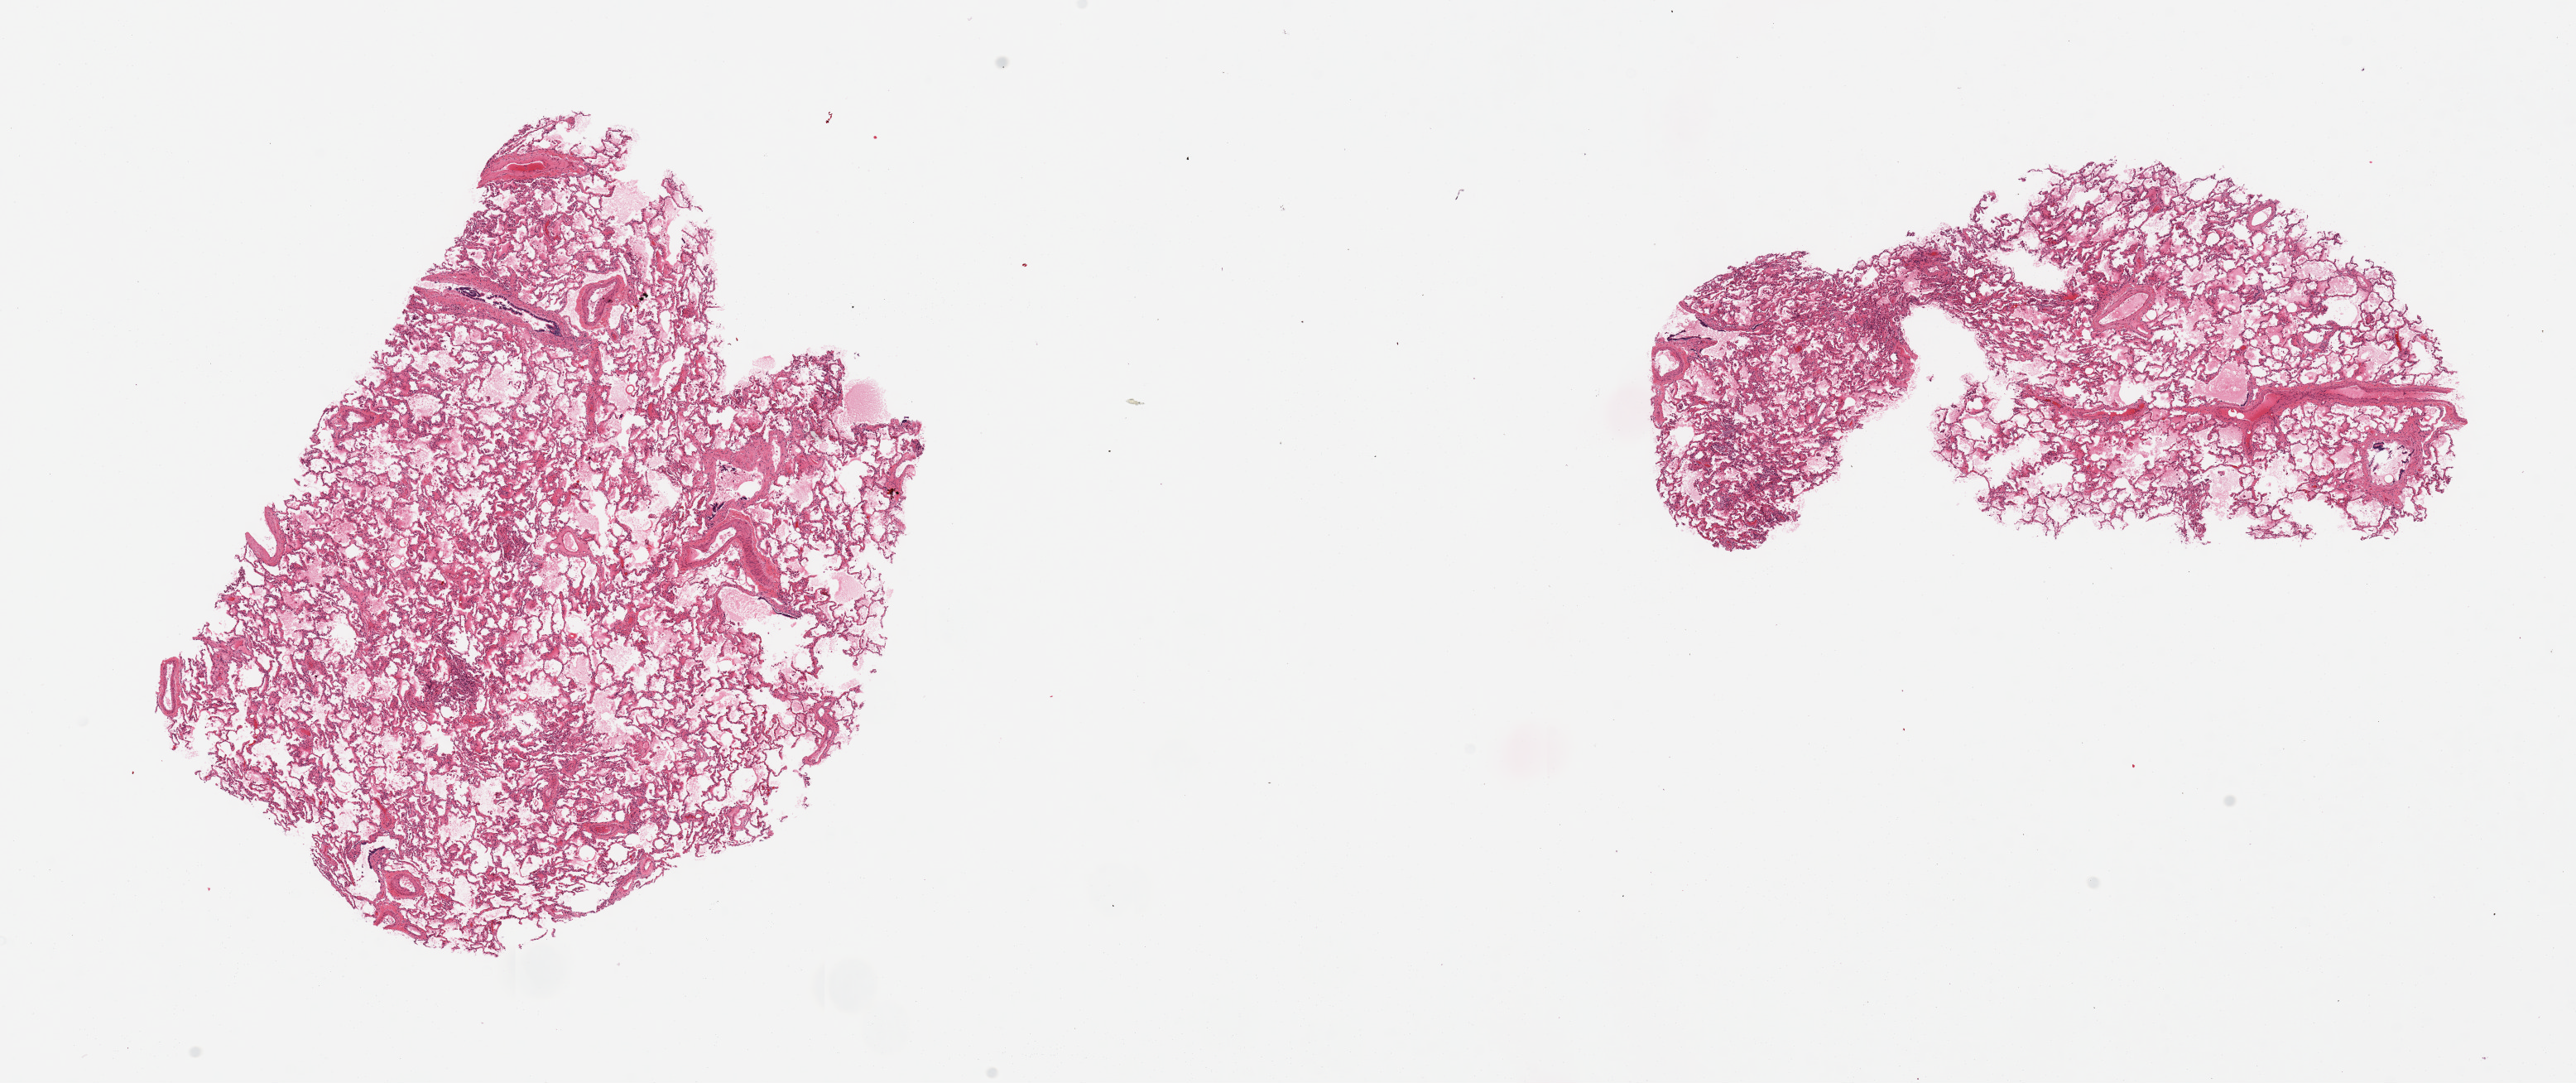
Digitized H&E-stained section, brightfield, a low-resolution overview of the entire scanned area, about 24.6 x 10.3 mm (acquisition: 20x scan); PAXgene-fixed paraffin-embedded (PFPE) section; section of lung (target tissue); donor tissue sample. Donor: female.
Review note (as recorded): 2 pieces, minimal/mild congestion.